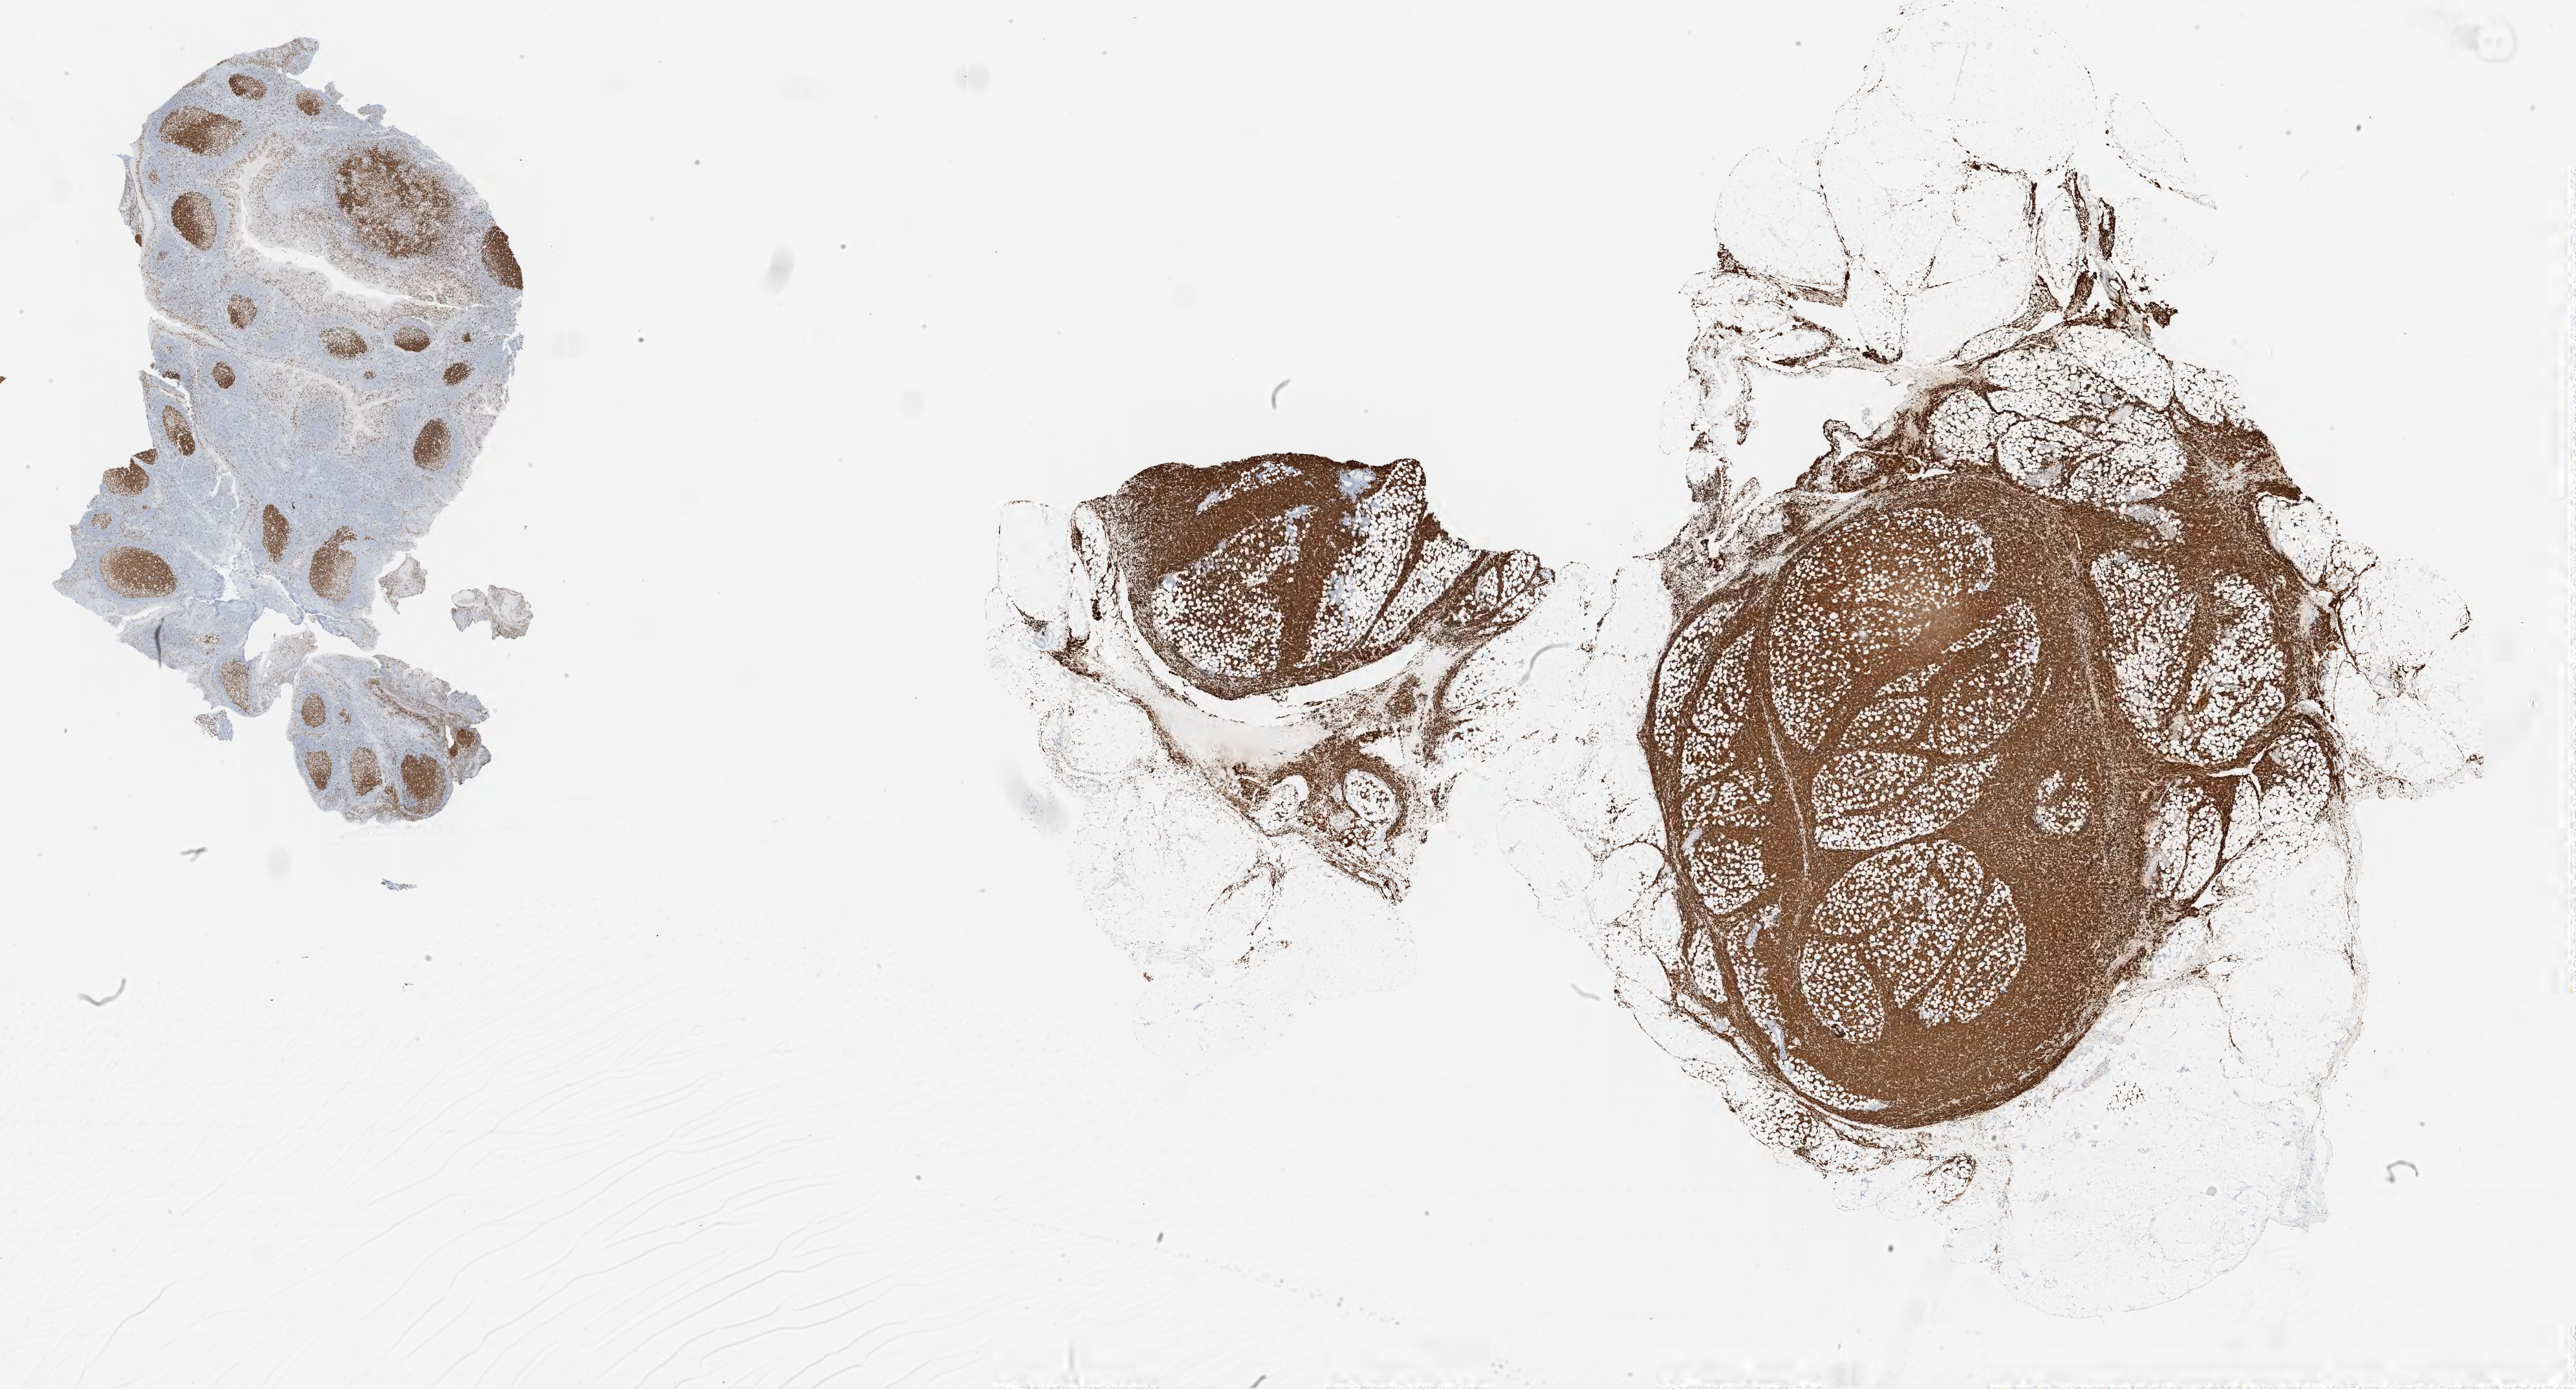
IHC for Ki-67, whole-slide image, shown as a low-resolution overview of the whole scanned area (about 32.0 x 17.2 mm). Tumor tissue. Patient: male, age 24 years.
• histologic diagnosis: Burkitt lymphoma, NOS